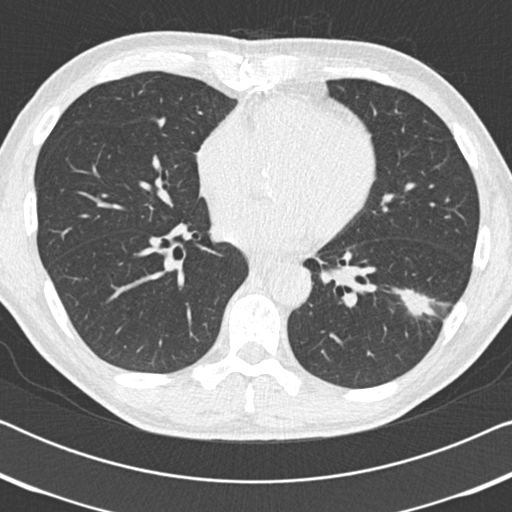
Low-dose screening chest CT, one axial slice; slice 81 of 186 in the series (ordered by position); reconstruction kernel B30f; 120 kVp; lung window (W 1500 / L -600 HU); 512 × 512 image matrix, field of view 330 × 330 mm.
Structures marked on this image (expert manual segmentation):
- lesion 1 (tumor, lower lobe of left lung): box from (x=402, y=293) to (x=434, y=316) px